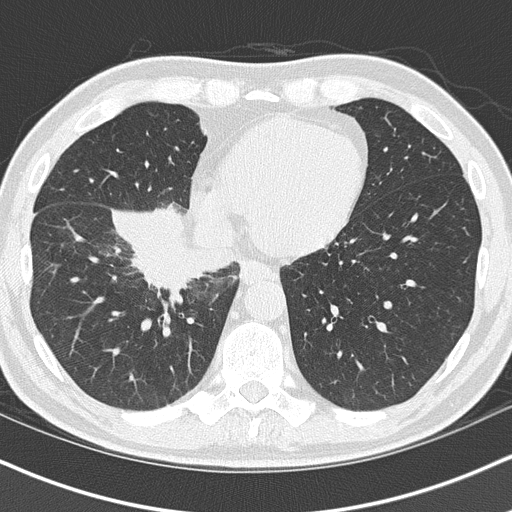
Low-dose screening chest CT, one axial slice. Position 40 of 151 along the scan axis. Reconstruction kernel B50f. Lung window (W 1500 / L -600 HU). 512 × 512 image matrix, field of view 320 × 320 mm.
Annotated regions visible in this slice (outlined manually by an expert reader):
- lesion 1 (tumor, hilum of right lung): bounding box (x1, y1, x2, y2) in pixels: (130, 235, 217, 286)